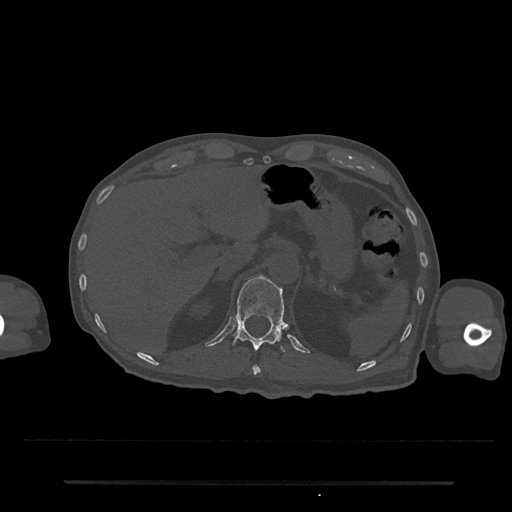
CT including the spine, one axial slice; slice 197 of 797 in the series (ordered by position); reconstruction kernel Br40s/3; 120 kVp; bone window (W 1800 / L 400 HU); 512 × 512 image matrix, field of view 427 × 427 mm. Male patient, age 74 years. From the clinical record (not read from this slice): primary cancer: prostate.
Structures marked on this image (semi-automatic segmentation, software-assisted and operator-edited):
- T11 vertebra: box from (x=252, y=365) to (x=261, y=375) px
- T12 vertebra: (x=233, y=277)–(x=286, y=352)